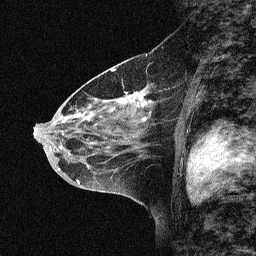
Breast MRI (dynamic contrast-enhanced), one sagittal slice. Slice 36 of 64 in the series (ordered by position). Dynamic contrast-enhanced study with each time point stored as its own series, time point 2 of 3 at this slice position (early post-contrast, ordered by acquisition time). 1.5 T. TE 4.5 ms, TR 11 ms. 2.06 mm slice thickness. 256 × 256 image matrix, field of view 200 × 200 mm. Patient: female, 46 years. From the clinical record (not read from this slice): setting: breast cancer imaged before/during neoadjuvant chemotherapy; receptor status: HER2-positive.
Outlined on this slice (semi-automatically segmented with operator editing):
- analysis volume of interest (the breast-tissue region the enhancement analysis was run in; not a lesion): bounding box <46,51,180,169> (left, top, right, bottom; pixels)
- tumour enhancement mask (voxels above the 90 % enhancement threshold inside the analysis volume of interest): <121,94,146,105>